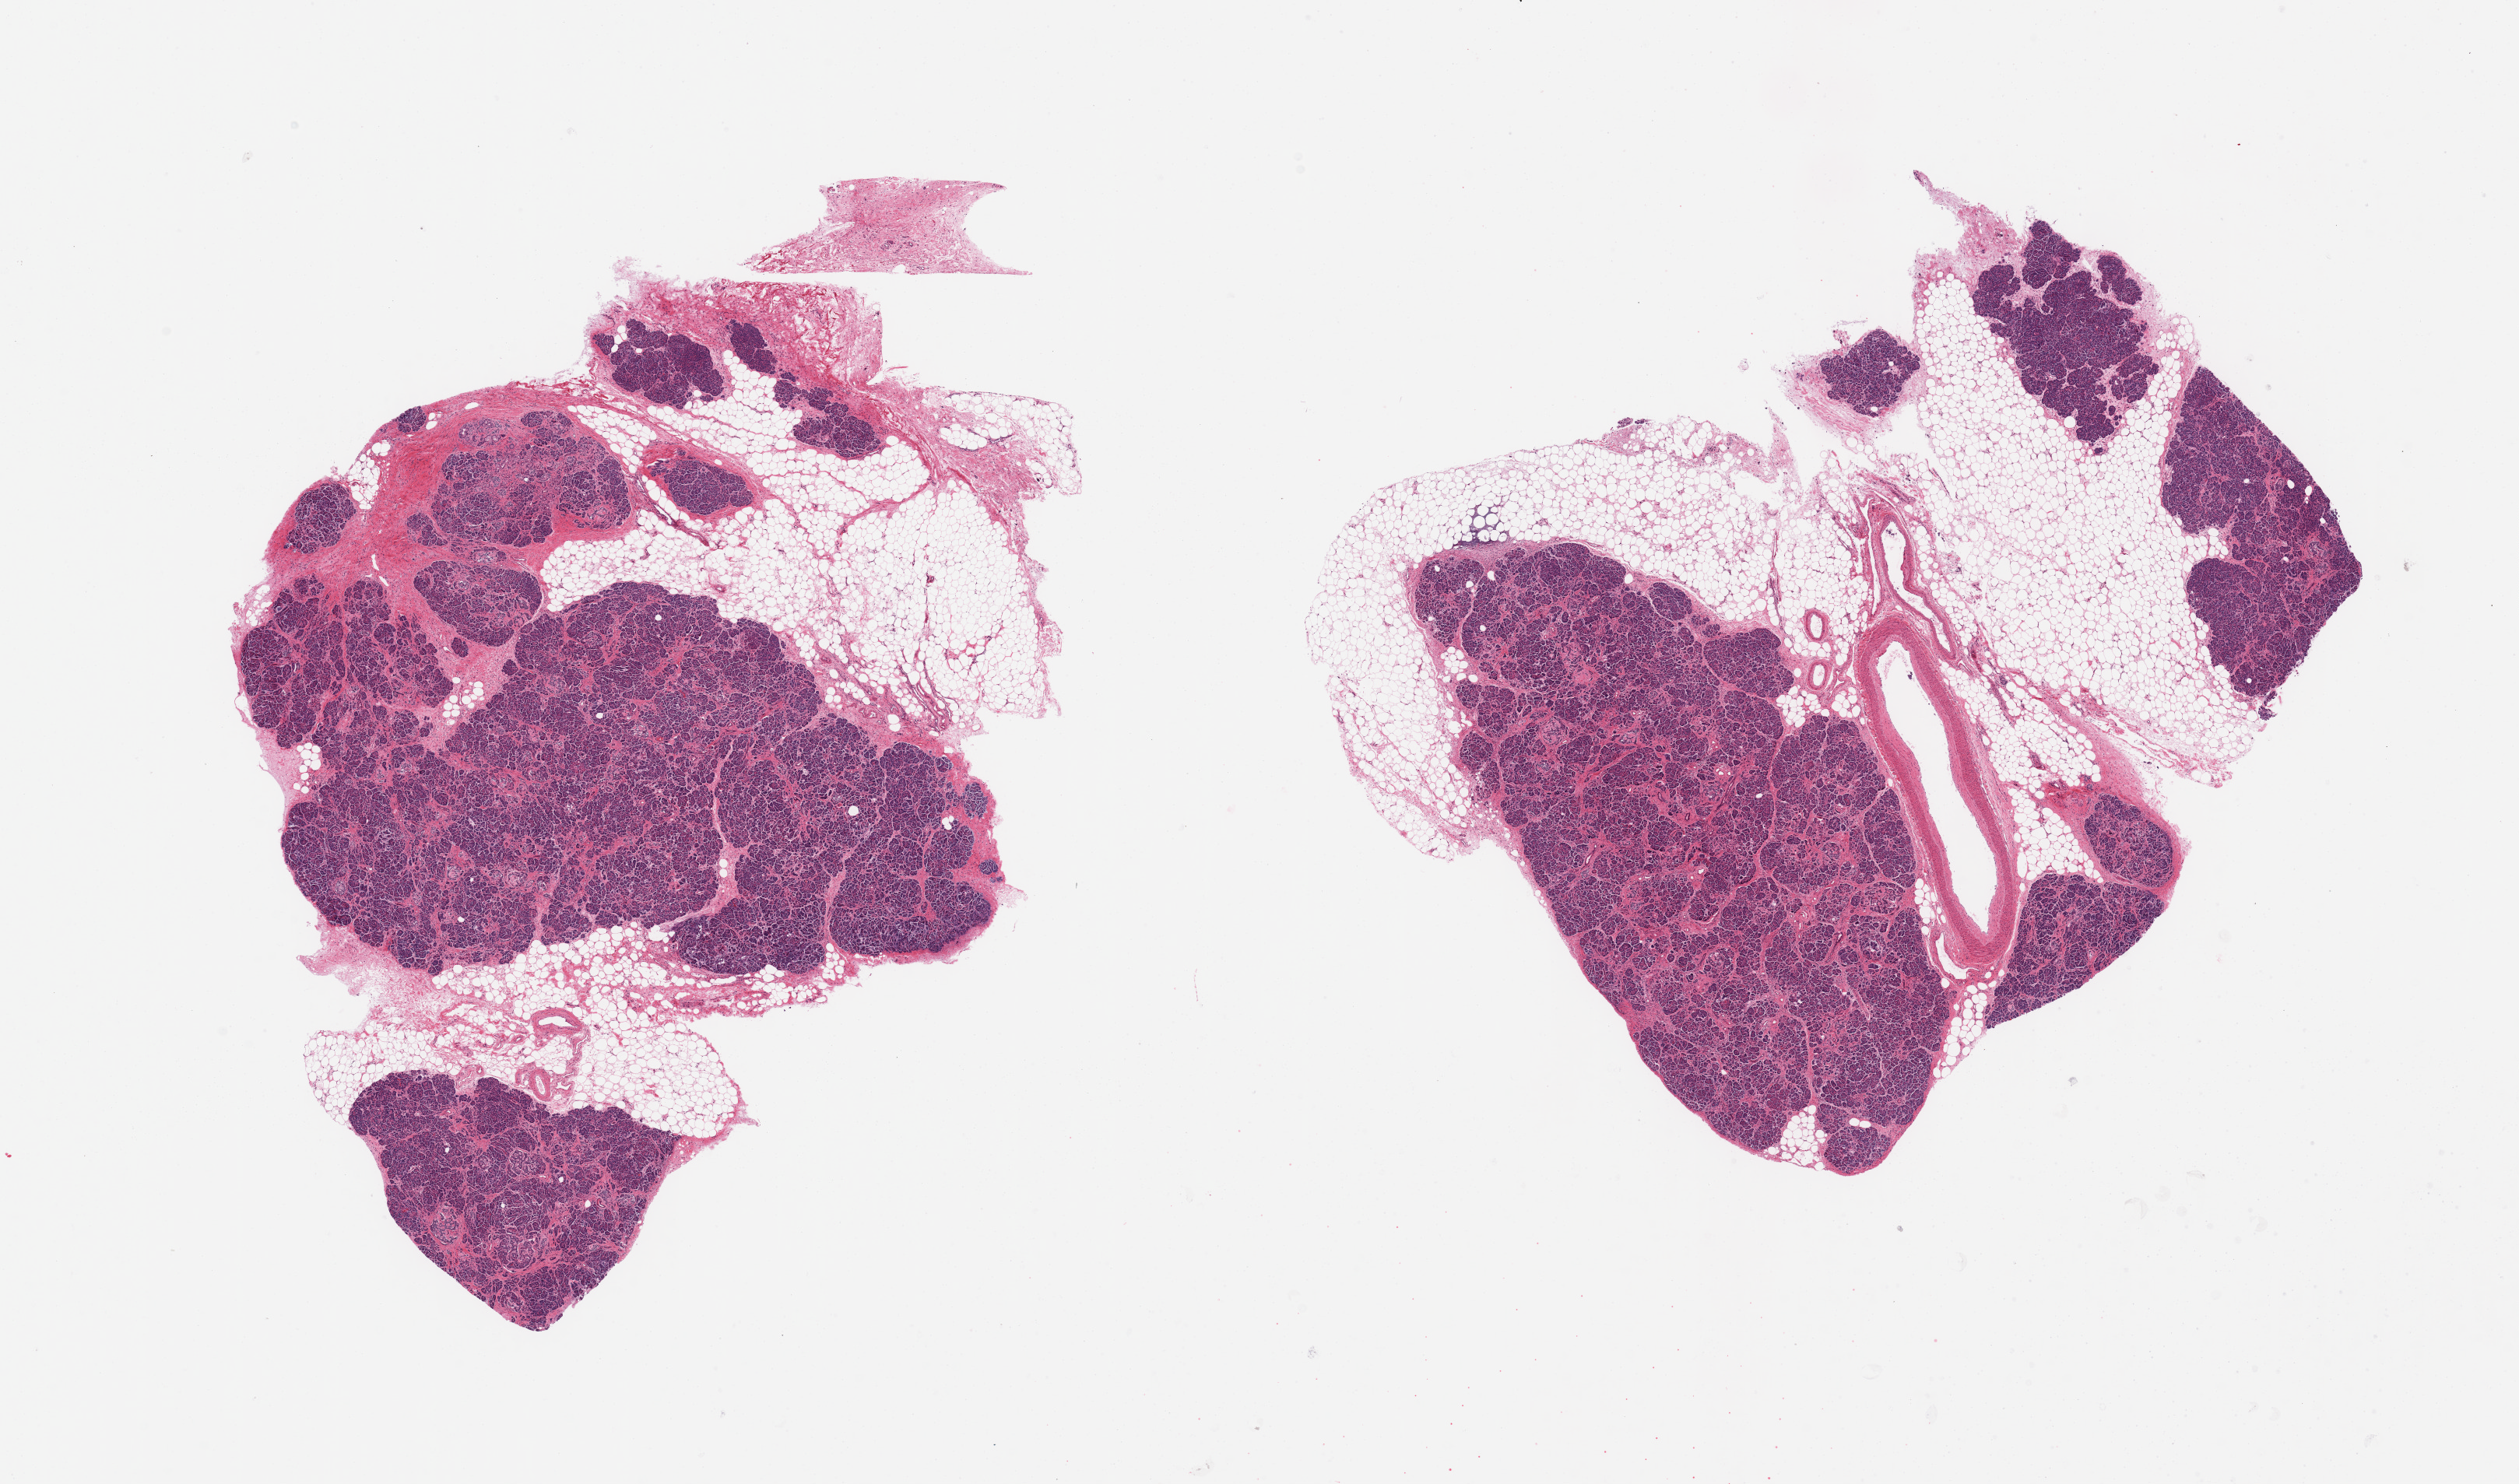
Whole-slide image, haematoxylin and eosin stain, brightfield, a low-resolution overview of the entire scanned area, about 25.6 x 15.1 mm (from a 20x scan), PAXgene-fixed paraffin-embedded (PFPE) section, target tissue: pancreas, donor tissue sample. Donor sex: male.
Reviewer comment on this tissue sample: 2 pieces, moderately advanced saponification overall; Islets still visible but moderately degenerating.